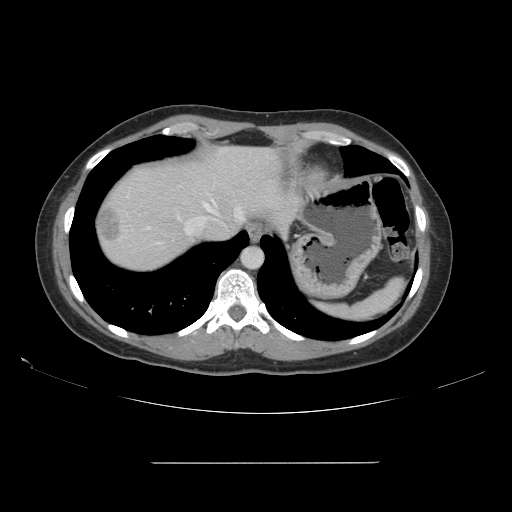
Contrast-enhanced abdominal CT, one axial slice. Intravenous contrast given. Soft-tissue window (W 400 / L 40 HU). 2.5 mm slice thickness. 512 × 512 image matrix, field of view 421 × 421 mm. Female patient, age 46 years. Case-level facts recorded for this patient, not image findings: diagnosis: colorectal cancer liver metastases, imaged before liver resection; multiple liver metastases: yes; largest metastasis: 3 cm; chemotherapy before resection: no.
Outlined on this slice (outlined manually by an expert reader):
- hepatic veins: bounding box (x1, y1, x2, y2) in pixels: (186, 204, 243, 233)
- liver: (95, 147, 280, 272)
- planned liver remnant (the part of the liver to remain after resection): (108, 148, 279, 235)
- liver metastasis: (99, 206, 122, 246)